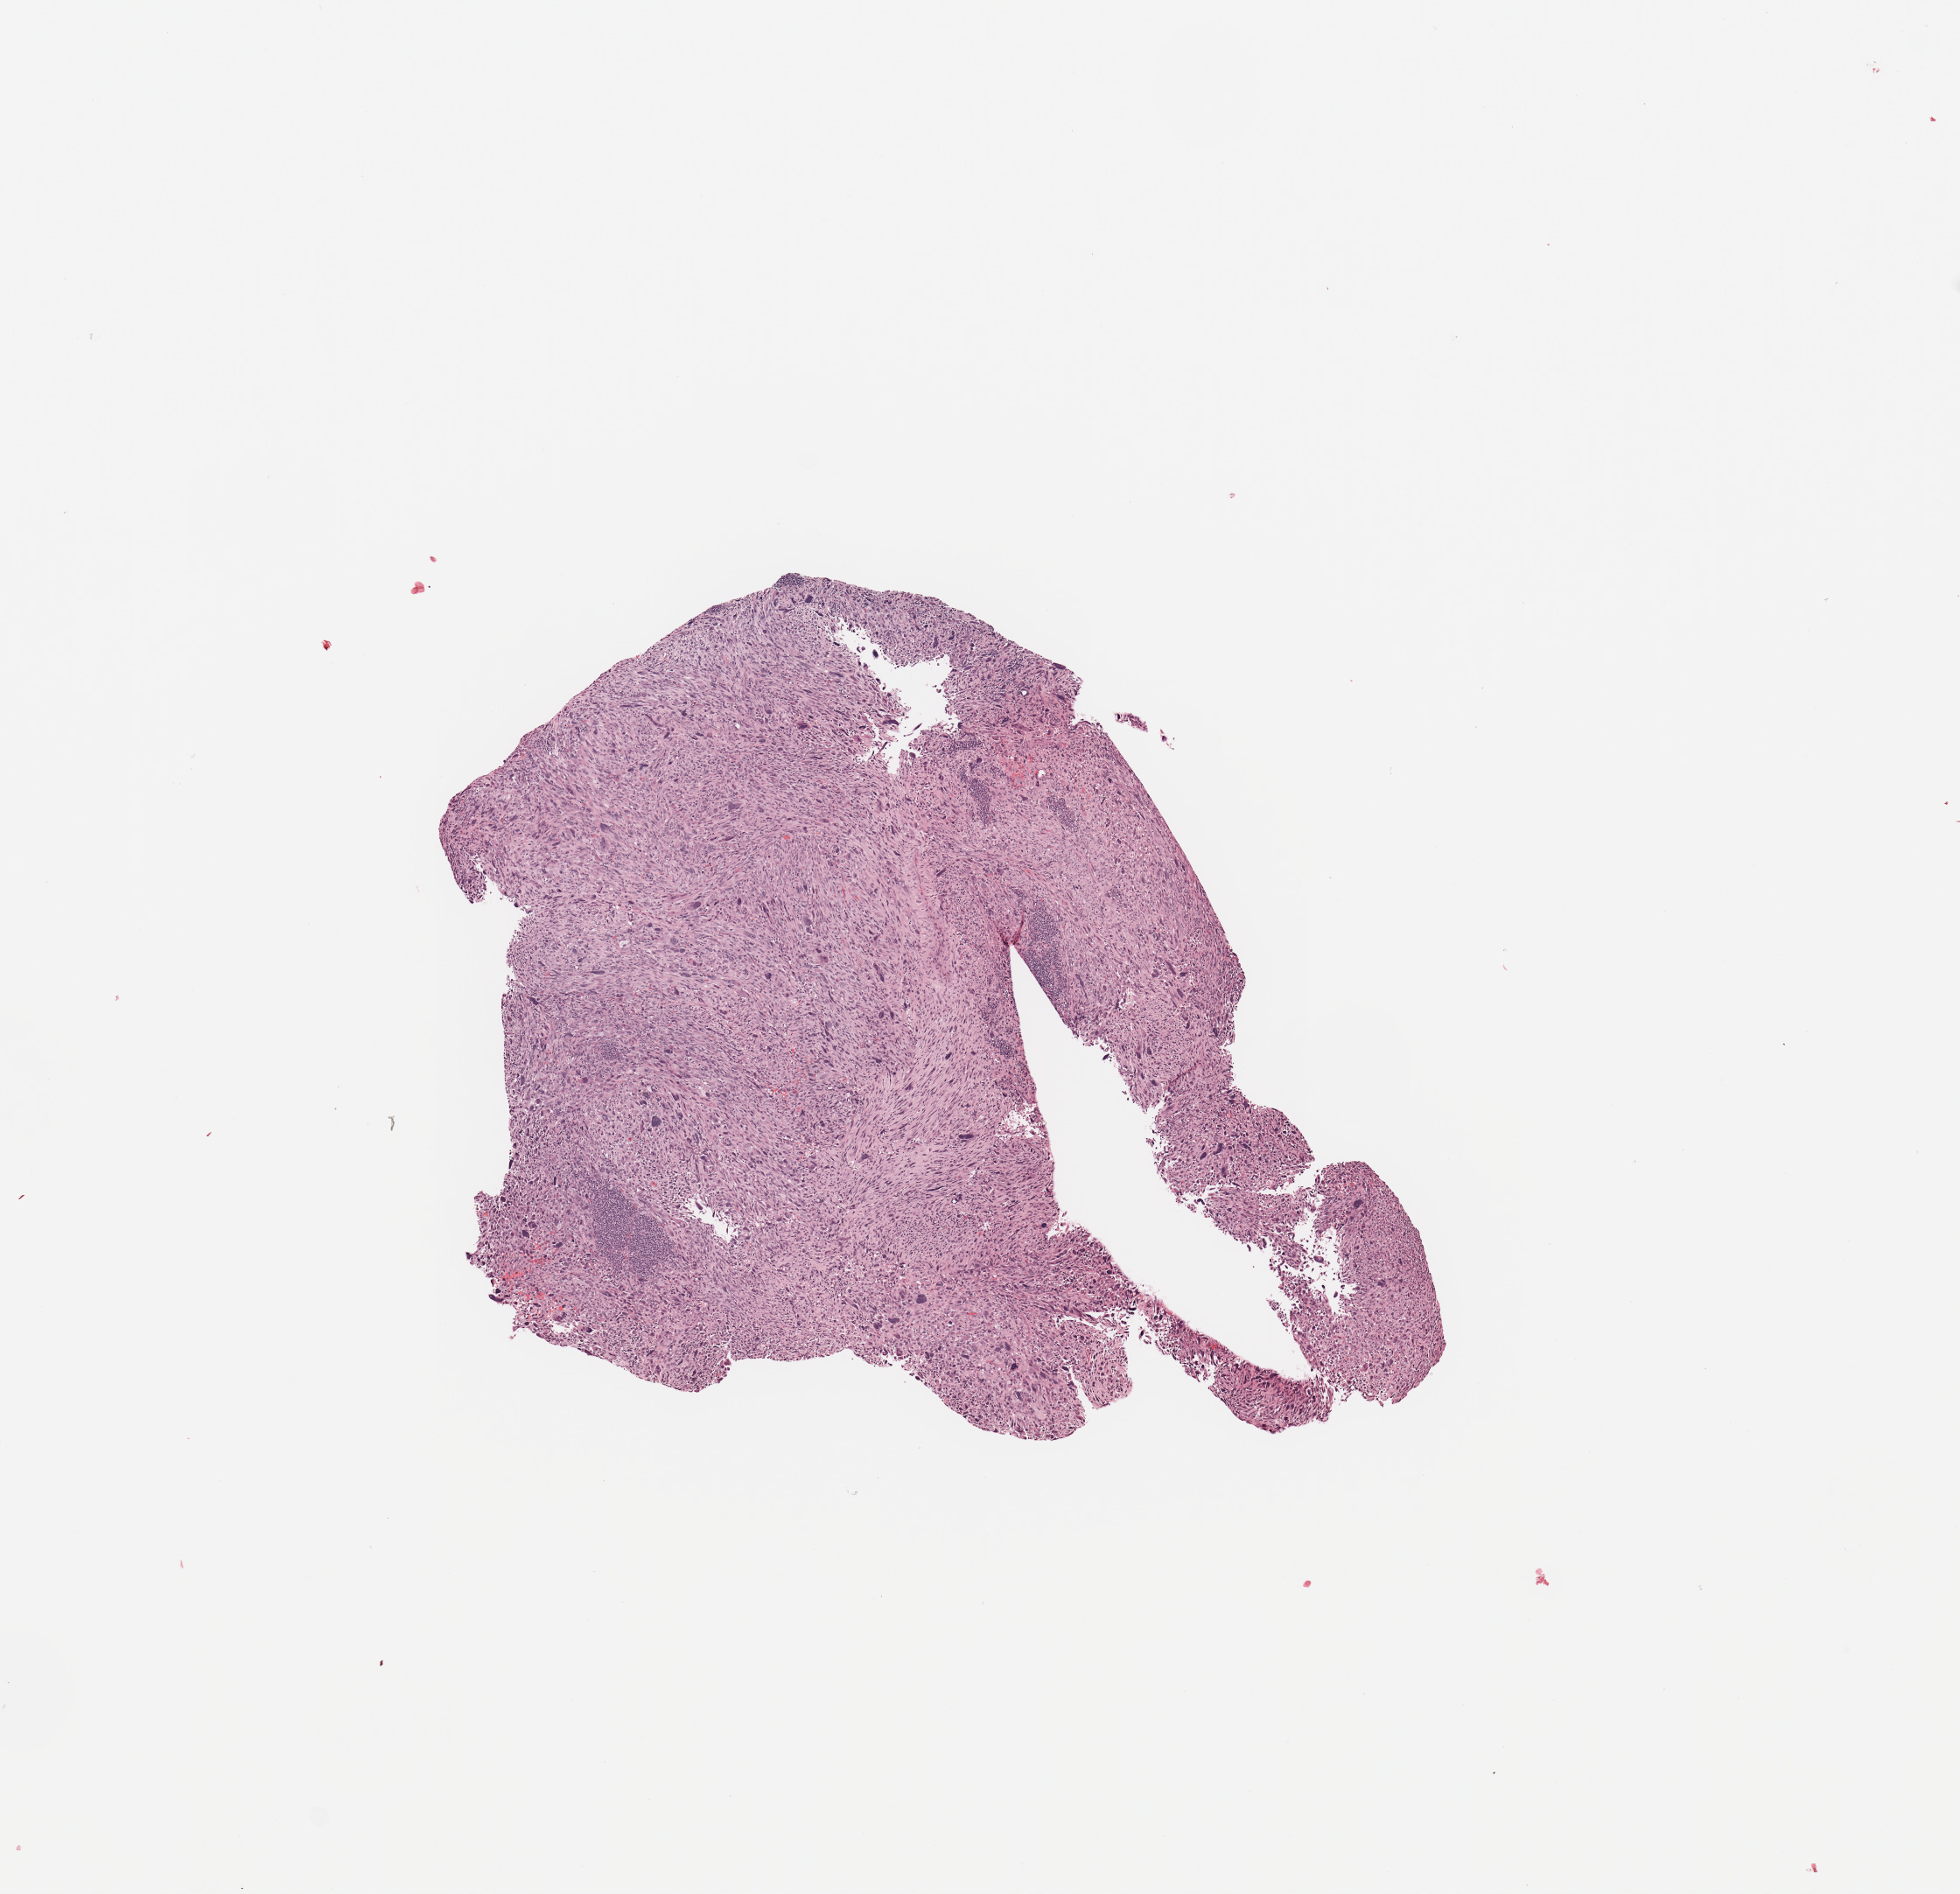
H&E whole-slide image — low-resolution overview of the scanned area, about 8.9 x 8.6 mm (acquisition: 20x scan); tumour tissue sample. Patient: female, age 67 years.
Patient diagnosis (cohort enrolment): sarcoma (site not recorded at cohort level). Primary tumour site (as recorded): upper extremity.